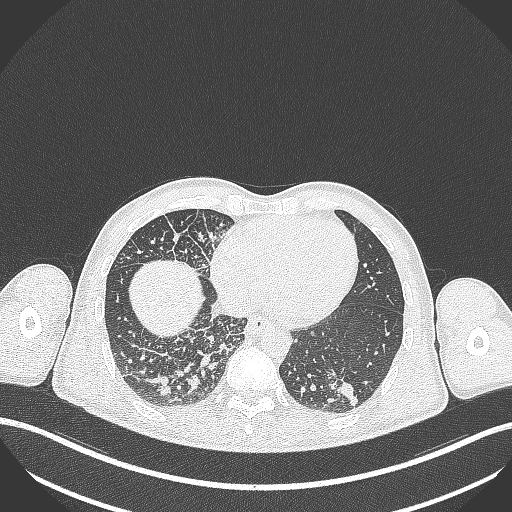
Chest CT, one axial slice; position 91 of 348 along the scan axis; 120 kVp; lung window (W 1500 / L -600 HU); 1 mm slice thickness; 512 × 512 image matrix, field of view 400 × 400 mm. Patient: male, 49 years. From the clinical record (not read from this slice): clinical TNM (as recorded): T2b N1 M0.
Structures marked on this image (rectangle marked by the reading radiologist):
- lung tumour (recorded histology: adenocarcinoma): bounding box <322,367,362,409> (left, top, right, bottom; pixels)